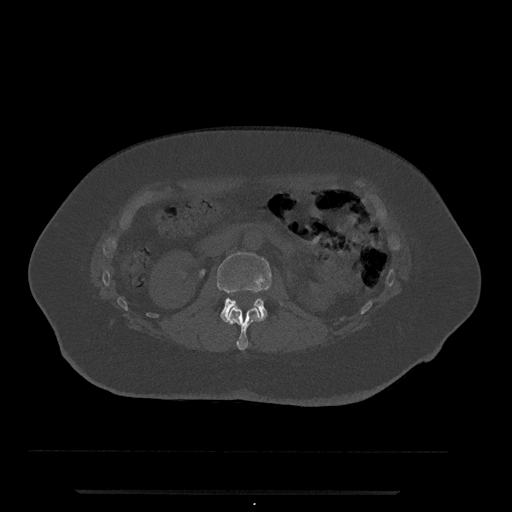
CT including the spine, one axial slice; position 64 of 797 along the scan axis; bone window (W 1800 / L 400 HU); 0.5 mm slice thickness; 512 × 512 image matrix. Female patient, age 51 years. From the clinical record (not read from this slice): primary cancer: neuro.
Structures marked on this image (semi-automatic segmentation, software-assisted and operator-edited):
- L1 vertebra: bounding box (x1, y1, x2, y2) in pixels: (225, 307, 261, 351)
- L2 vertebra: (217, 252, 271, 323)